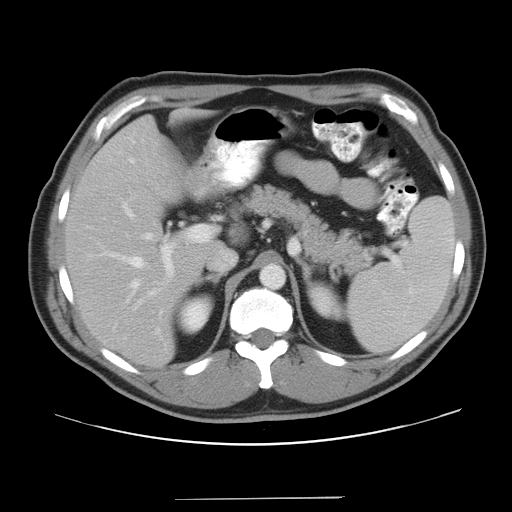
Contrast-enhanced abdominal CT, one axial slice. Slice 25 of 37 in the series (ordered by position). Intravenous contrast given. Soft-tissue window (W 400 / L 40 HU). 7.5 mm slice thickness. 512 × 512 image matrix. Male patient, age 46 years. From the clinical record (not read from this slice): diagnosis: colorectal cancer liver metastases, imaged before liver resection; multiple liver metastases: yes; largest metastasis: 1 cm; disease in both lobes: no.
Structures marked on this image (outlined manually by an expert reader):
- hepatic veins: box from (x=109, y=252) to (x=149, y=303) px
- liver: (x=68, y=119)–(x=210, y=364)
- planned liver remnant (the part of the liver to remain after resection): (x=68, y=118)–(x=210, y=364)
- portal vein (with intrahepatic branches): (x=123, y=202)–(x=215, y=334)